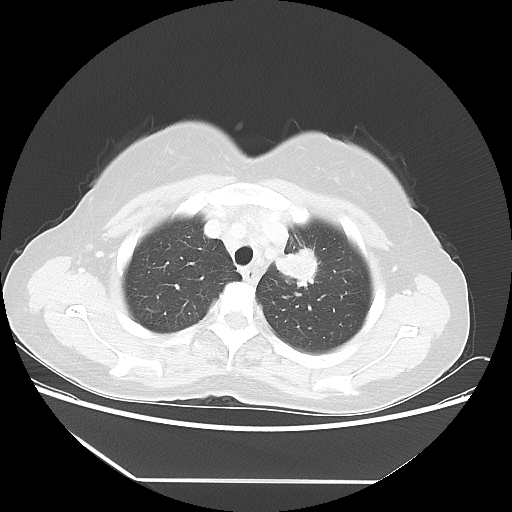
Chest CT, one axial slice; slice 43 of 52 in the series (ordered by position); 100 kVp; lung window (W 1500 / L -600 HU); 5 mm slice thickness; 512 × 512 image matrix. Female patient, age 50 years. From the clinical record (not read from this slice): clinical TNM (as recorded): T2 N3 M0.
Outlined on this slice (bounding box drawn by a radiologist):
- lung tumour (recorded histology: adenocarcinoma): box from (x=263, y=233) to (x=325, y=294) px